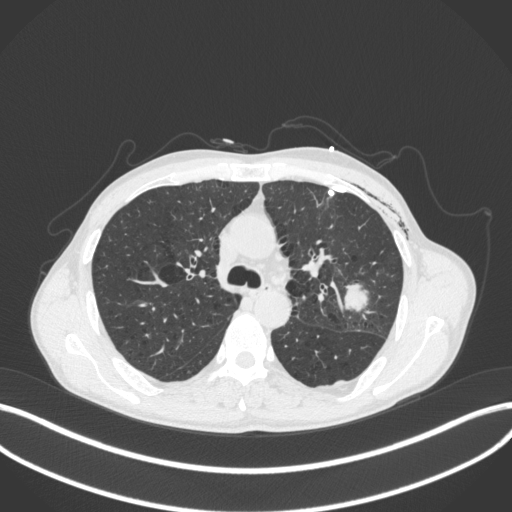
Chest CT, one axial slice; slice 267 of 416 in the series (ordered by position); reconstruction kernel B31f; 120 kVp; lung window (W 1500 / L -600 HU); 1 mm slice thickness; 512 × 512 image matrix, field of view 400 × 400 mm. Patient: male, 58 years. Case-level facts recorded for this patient, not image findings: clinical TNM (as recorded): T3 N0 M0.
Outlined on this slice (bounding box drawn by a radiologist):
- lung tumour (recorded histology: adenocarcinoma): bounding box (x1, y1, x2, y2) in pixels: (338, 278, 370, 314)